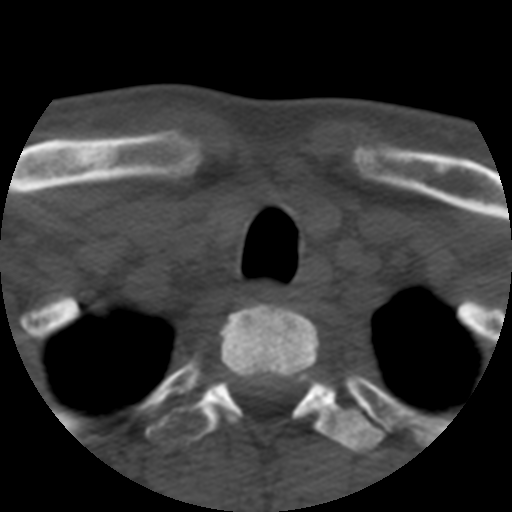
CT including the spine, one axial slice; slice 439 of 508 in the series (ordered by position); reconstruction kernel STANDARD; bone window (W 1800 / L 400 HU); 512 × 512 image matrix, field of view 160 × 160 mm. Patient age 57 years. Case-level facts recorded for this patient, not image findings: primary cancer: prostate.
Annotated regions visible in this slice (semi-automatically segmented with operator editing):
- T1 vertebra: bounding box <219,304,320,421> (left, top, right, bottom; pixels)
- T2 vertebra: <145,366,384,460>